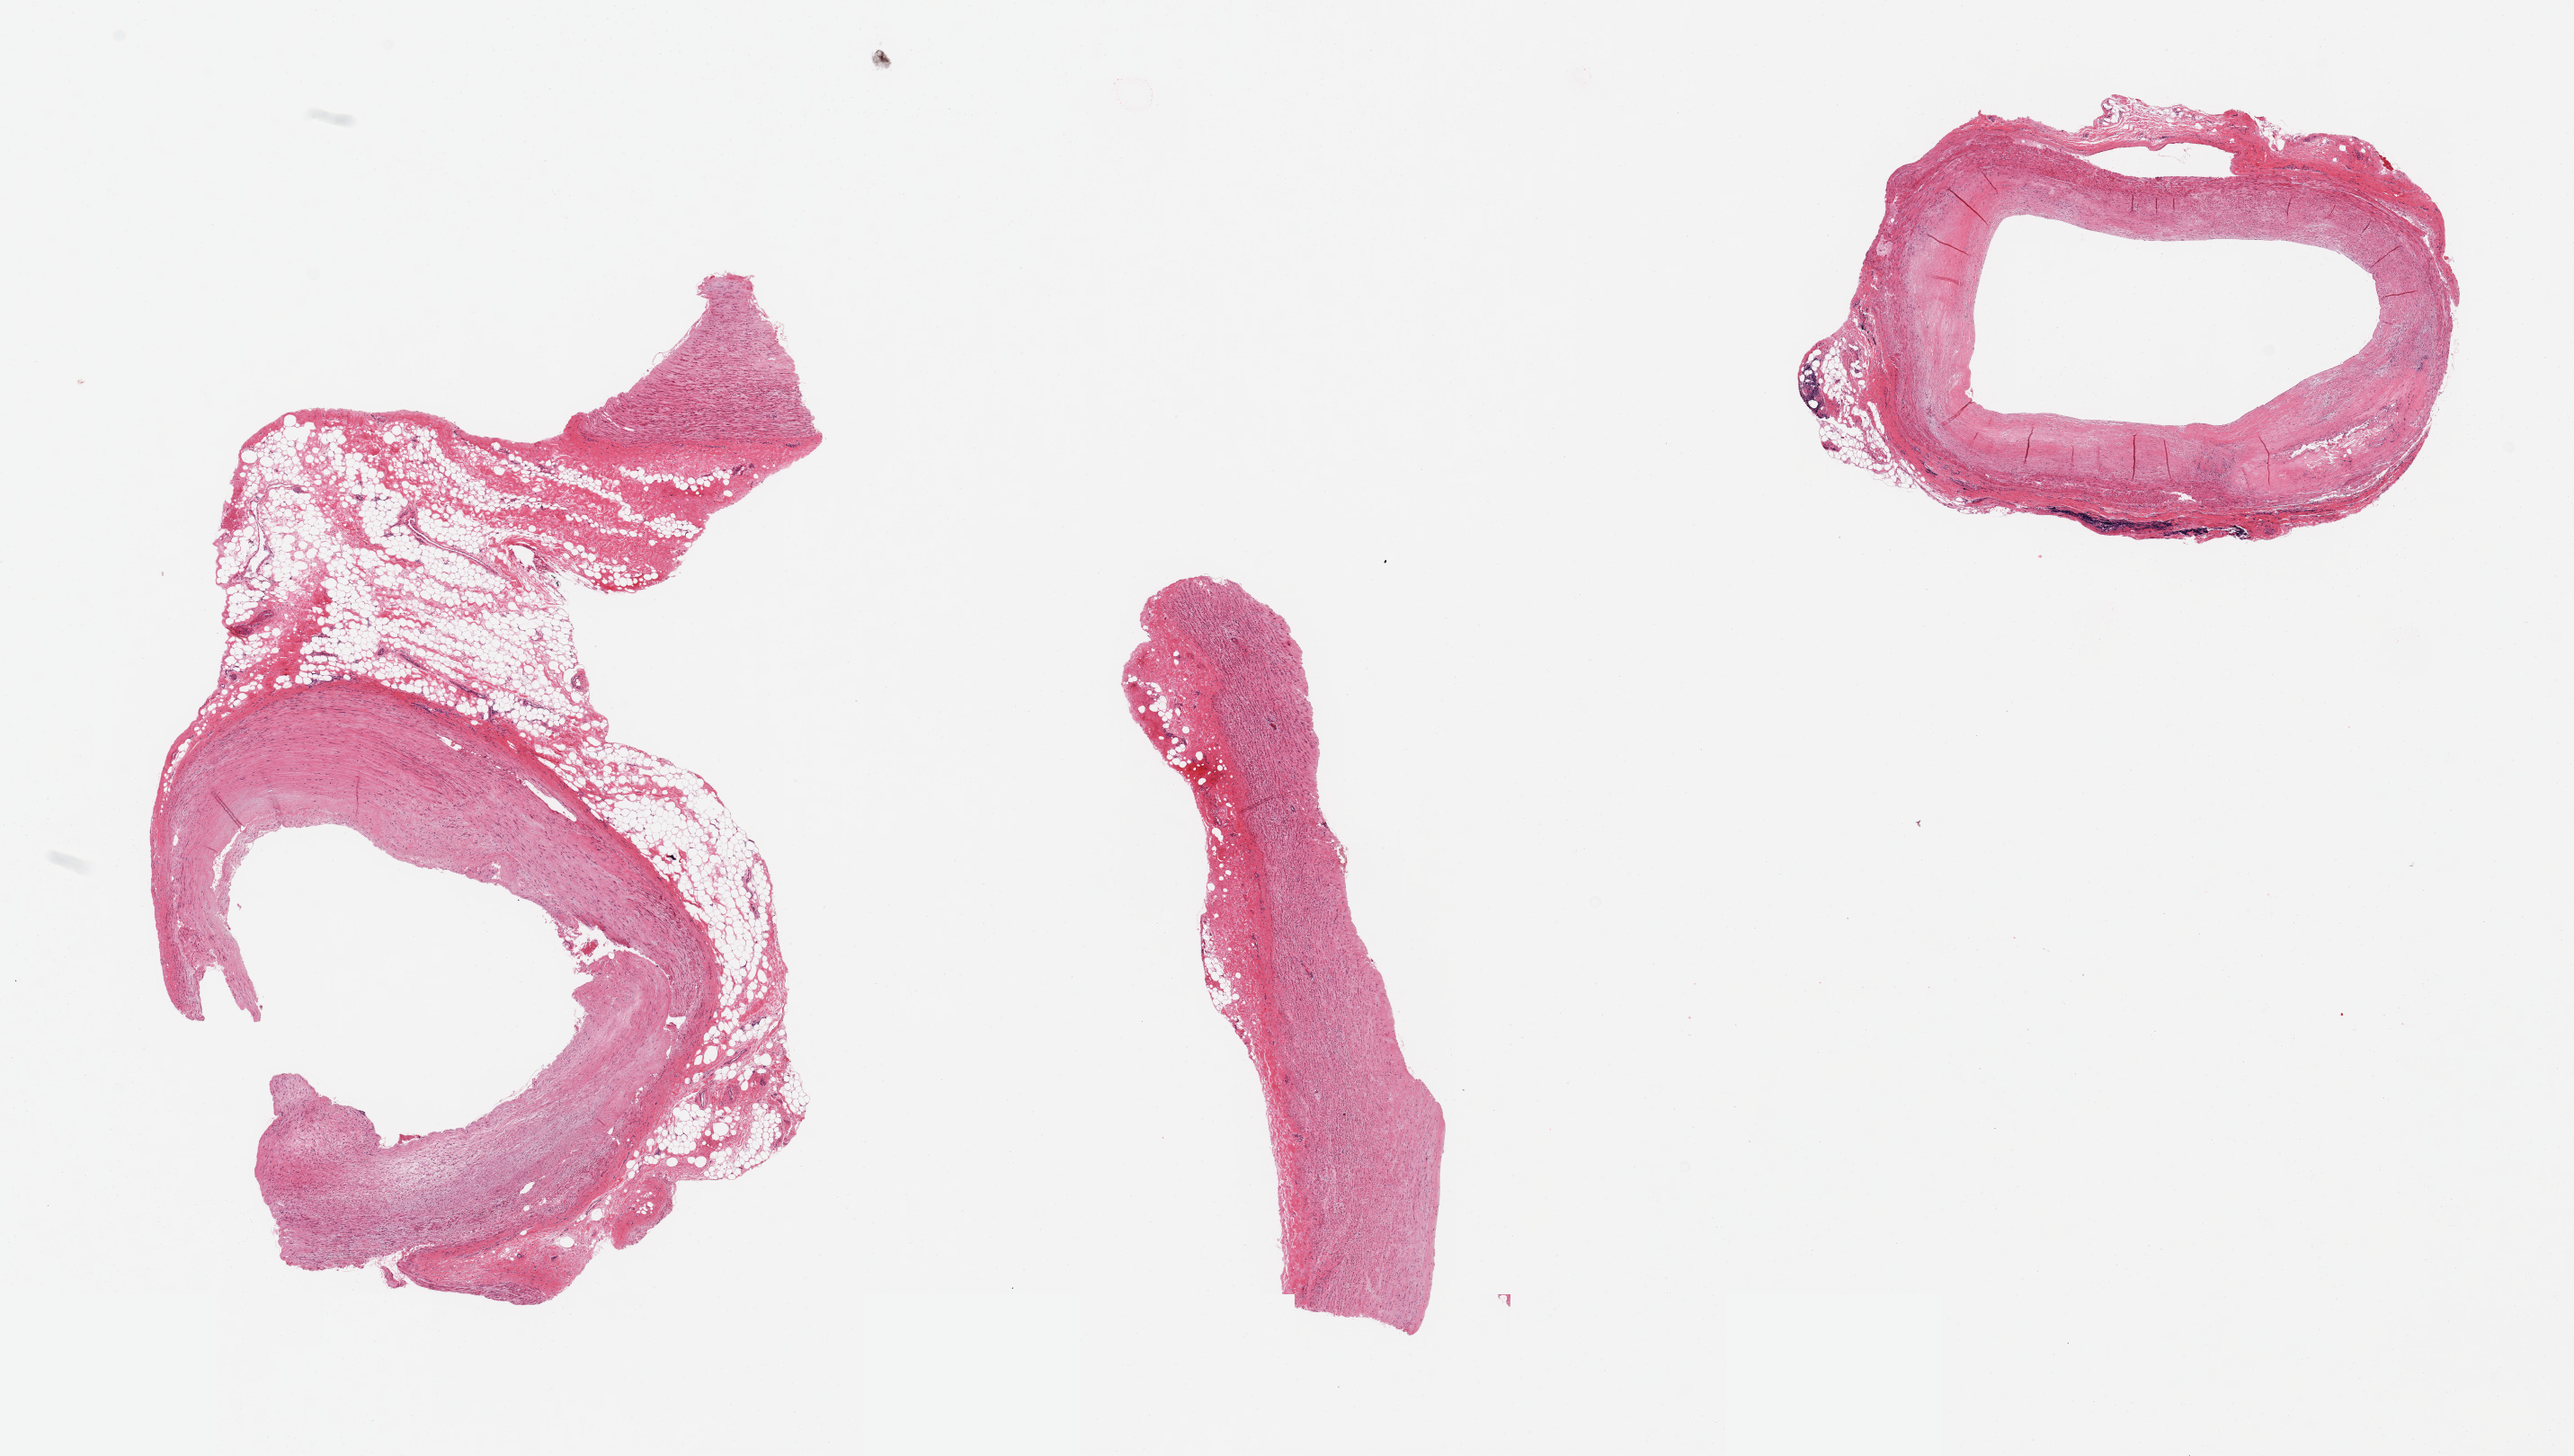
Whole-slide image, haematoxylin and eosin stain — a low-resolution overview of the entire scanned area, about 22.6 x 12.8 mm (from a 20x scan); PAXgene-fixed, paraffin-embedded tissue; target tissue: coronary artery; donor tissue sample. Female donor.
Reviewer comment on this tissue sample: 3 pieces (one vessel fragment--'fr'), adherent fat/connective tissue on one aliquot, ~2.5mm.